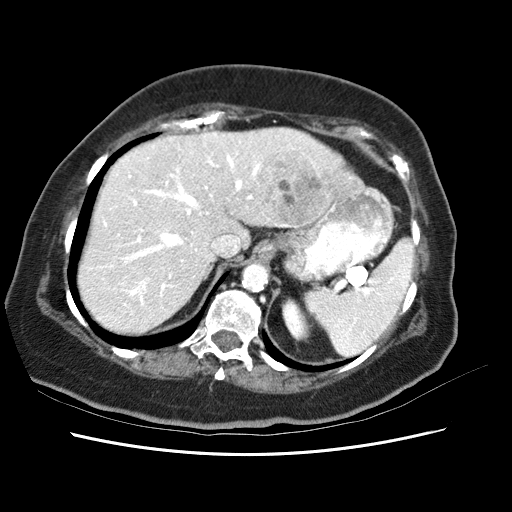
Contrast-enhanced abdominal CT (liver protocol), one axial slice. Position 46 of 62 along the scan axis. Soft-tissue window (W 400 / L 40 HU). 2.5 mm slice thickness. 512 × 512 image matrix, field of view 340 × 340 mm. Case-level facts recorded for this patient, not image findings: diagnosis: hepatocellular carcinoma (patient treated with transarterial chemoembolisation; whether this scan precedes or follows treatment is not stated here); TNM stage (as recorded): Stage-I; Child-Pugh class: B; tumour nodularity: uninodular.
Annotated regions visible in this slice (semi-automatic segmentation, software-assisted and operator-edited):
- liver parenchyma outside the tumour (the mass and vessels are separate outlines, so this box may not span the whole liver): bounding box (x1, y1, x2, y2) in pixels: (86, 128, 353, 326)
- mass: (253, 145, 326, 226)
- liver vessels: (112, 148, 332, 312)